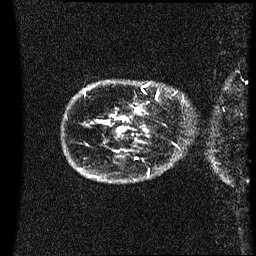
Breast MRI (dynamic contrast-enhanced), one sagittal slice; dynamic contrast-enhanced series, image 2 of 3 at this slice position (ordered by acquisition); 1.5 T; TE 4.2 ms, TR 8.4 ms; 2.2 mm slice thickness; 256 × 256 image matrix. Patient: female, 41 years. Case-level facts recorded for this patient, not image findings: setting: breast cancer imaged before/during neoadjuvant chemotherapy; receptor status: HER2-positive.
Outlined on this slice (semi-automatically segmented with operator editing):
- analysis volume of interest (the breast-tissue region the enhancement analysis was run in; not a lesion): bounding box <122,82,186,123> (left, top, right, bottom; pixels)
- tumour enhancement mask (voxels above the 70 % enhancement threshold inside the analysis volume of interest): <122,108,141,121>